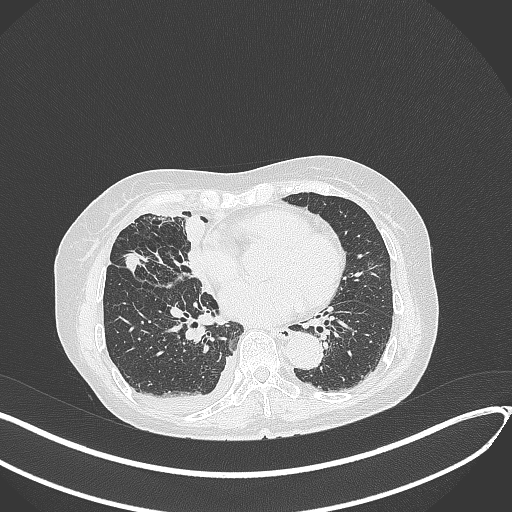
Chest CT, one axial slice; position 164 of 418 along the scan axis; reconstruction kernel B70f; lung window (W 1500 / L -600 HU); 512 × 512 image matrix, field of view 400 × 400 mm. Female patient, age 75 years. Case-level facts recorded for this patient, not image findings: clinical TNM (as recorded): T2a N3 M0.
Structures marked on this image (bounding box drawn by a radiologist):
- lung tumour (recorded histology: adenocarcinoma): bounding box [x1, y1, x2, y2] px = [123, 250, 143, 277]